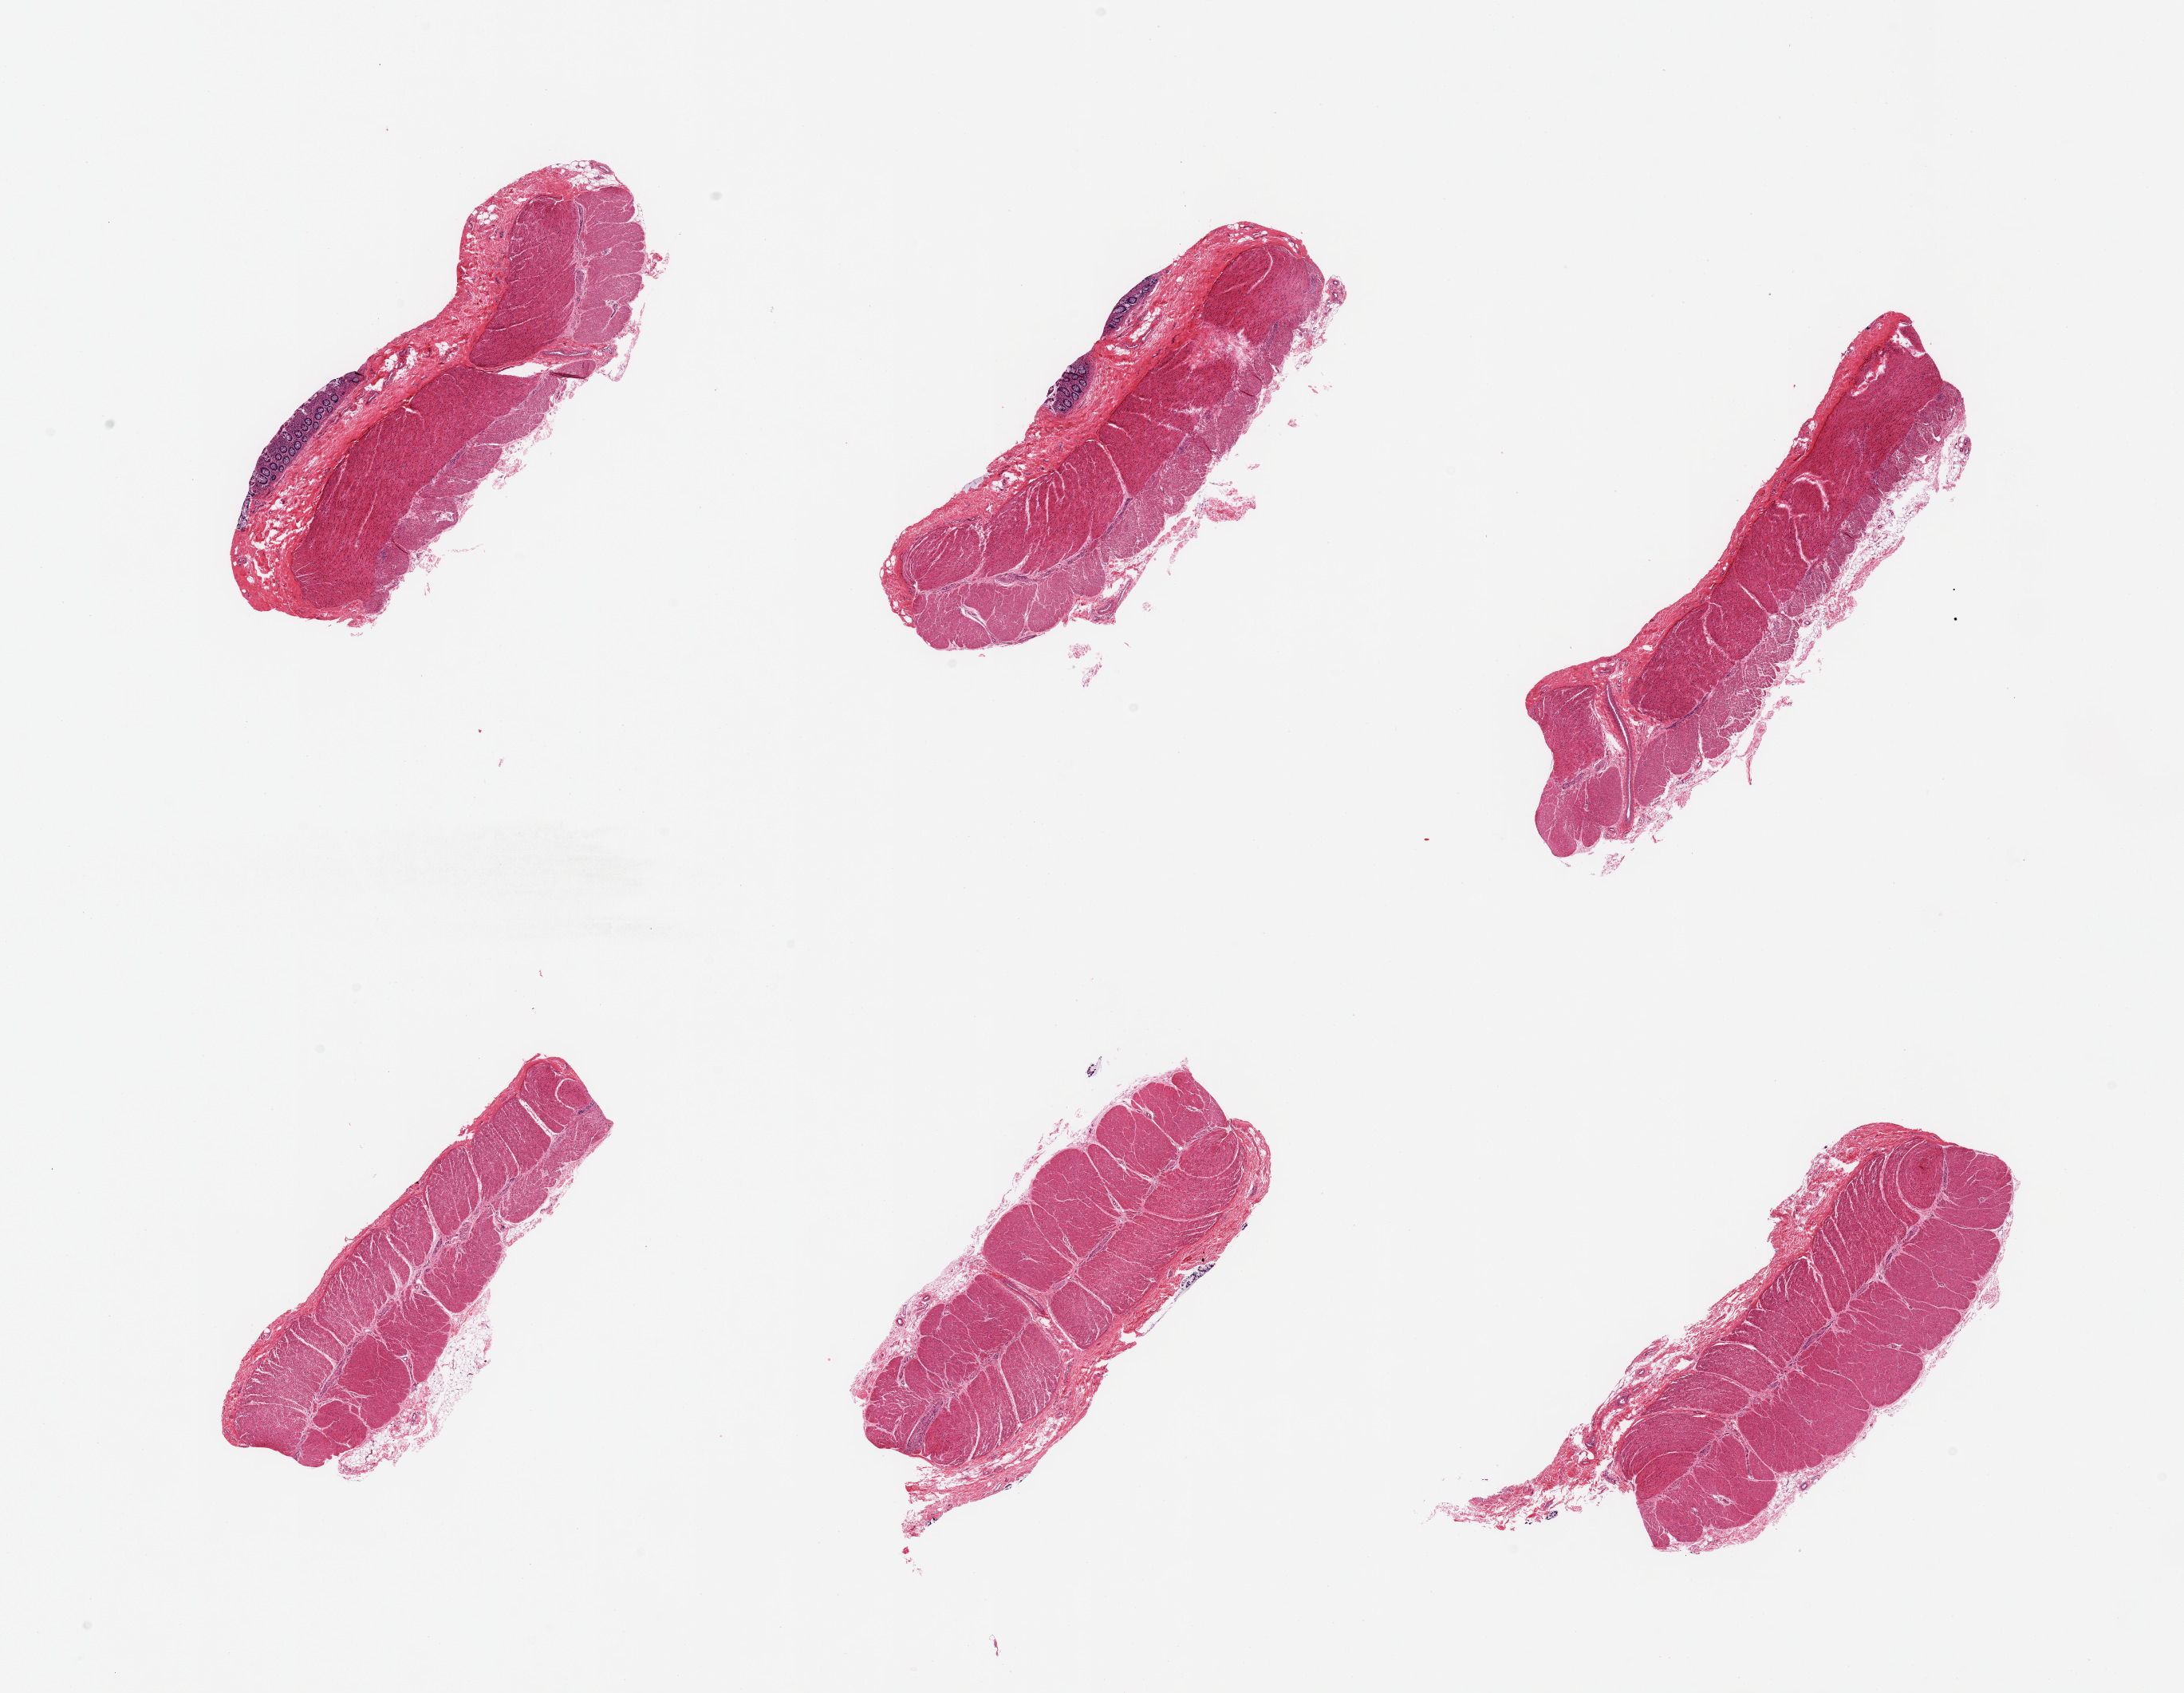
Whole-slide image, haematoxylin and eosin stain, a low-resolution overview of the entire scanned area, about 21.7 x 16.8 mm (acquisition: 20x scan). PAXgene-fixed, paraffin-embedded tissue. Target tissue: sigmoid colon. Donor tissue sample. Male donor.
Pathologist's review note for this sample: 6 pieces; well dissected except for several foci of mucosa on 2 of 6 pieces, occupying 5%.